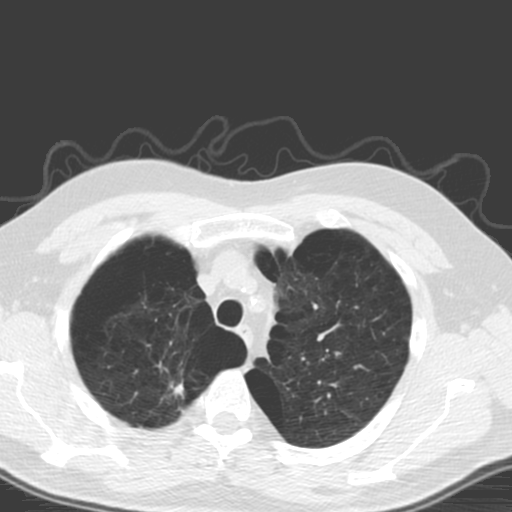
Axial slice from a low-dose chest CT screening exam; baseline screening round; lung window (W 1500 / L -600 HU); 3.2 mm slice thickness; slice 35 of 173 in the series. Male participant, aged 56 years at enrolment.
- Expert reader's lesion annotation, box from (x=141, y=354) to (x=208, y=433) px.
- Screening reader's record for this exam (one nodule recorded; not confirmed to be the boxed lesion): non-calcified nodule or mass ≥4 mm, right upper lobe, 20 × 12 mm, spiculated (stellate) margins, soft tissue attenuation.
- Later outcome: lung cancer diagnosed 205 days after this screen — large cell carcinoma, NOS, right upper lobe, poorly differentiated (G3), stage IA (AJCC 6th edition), 18 mm at pathology.